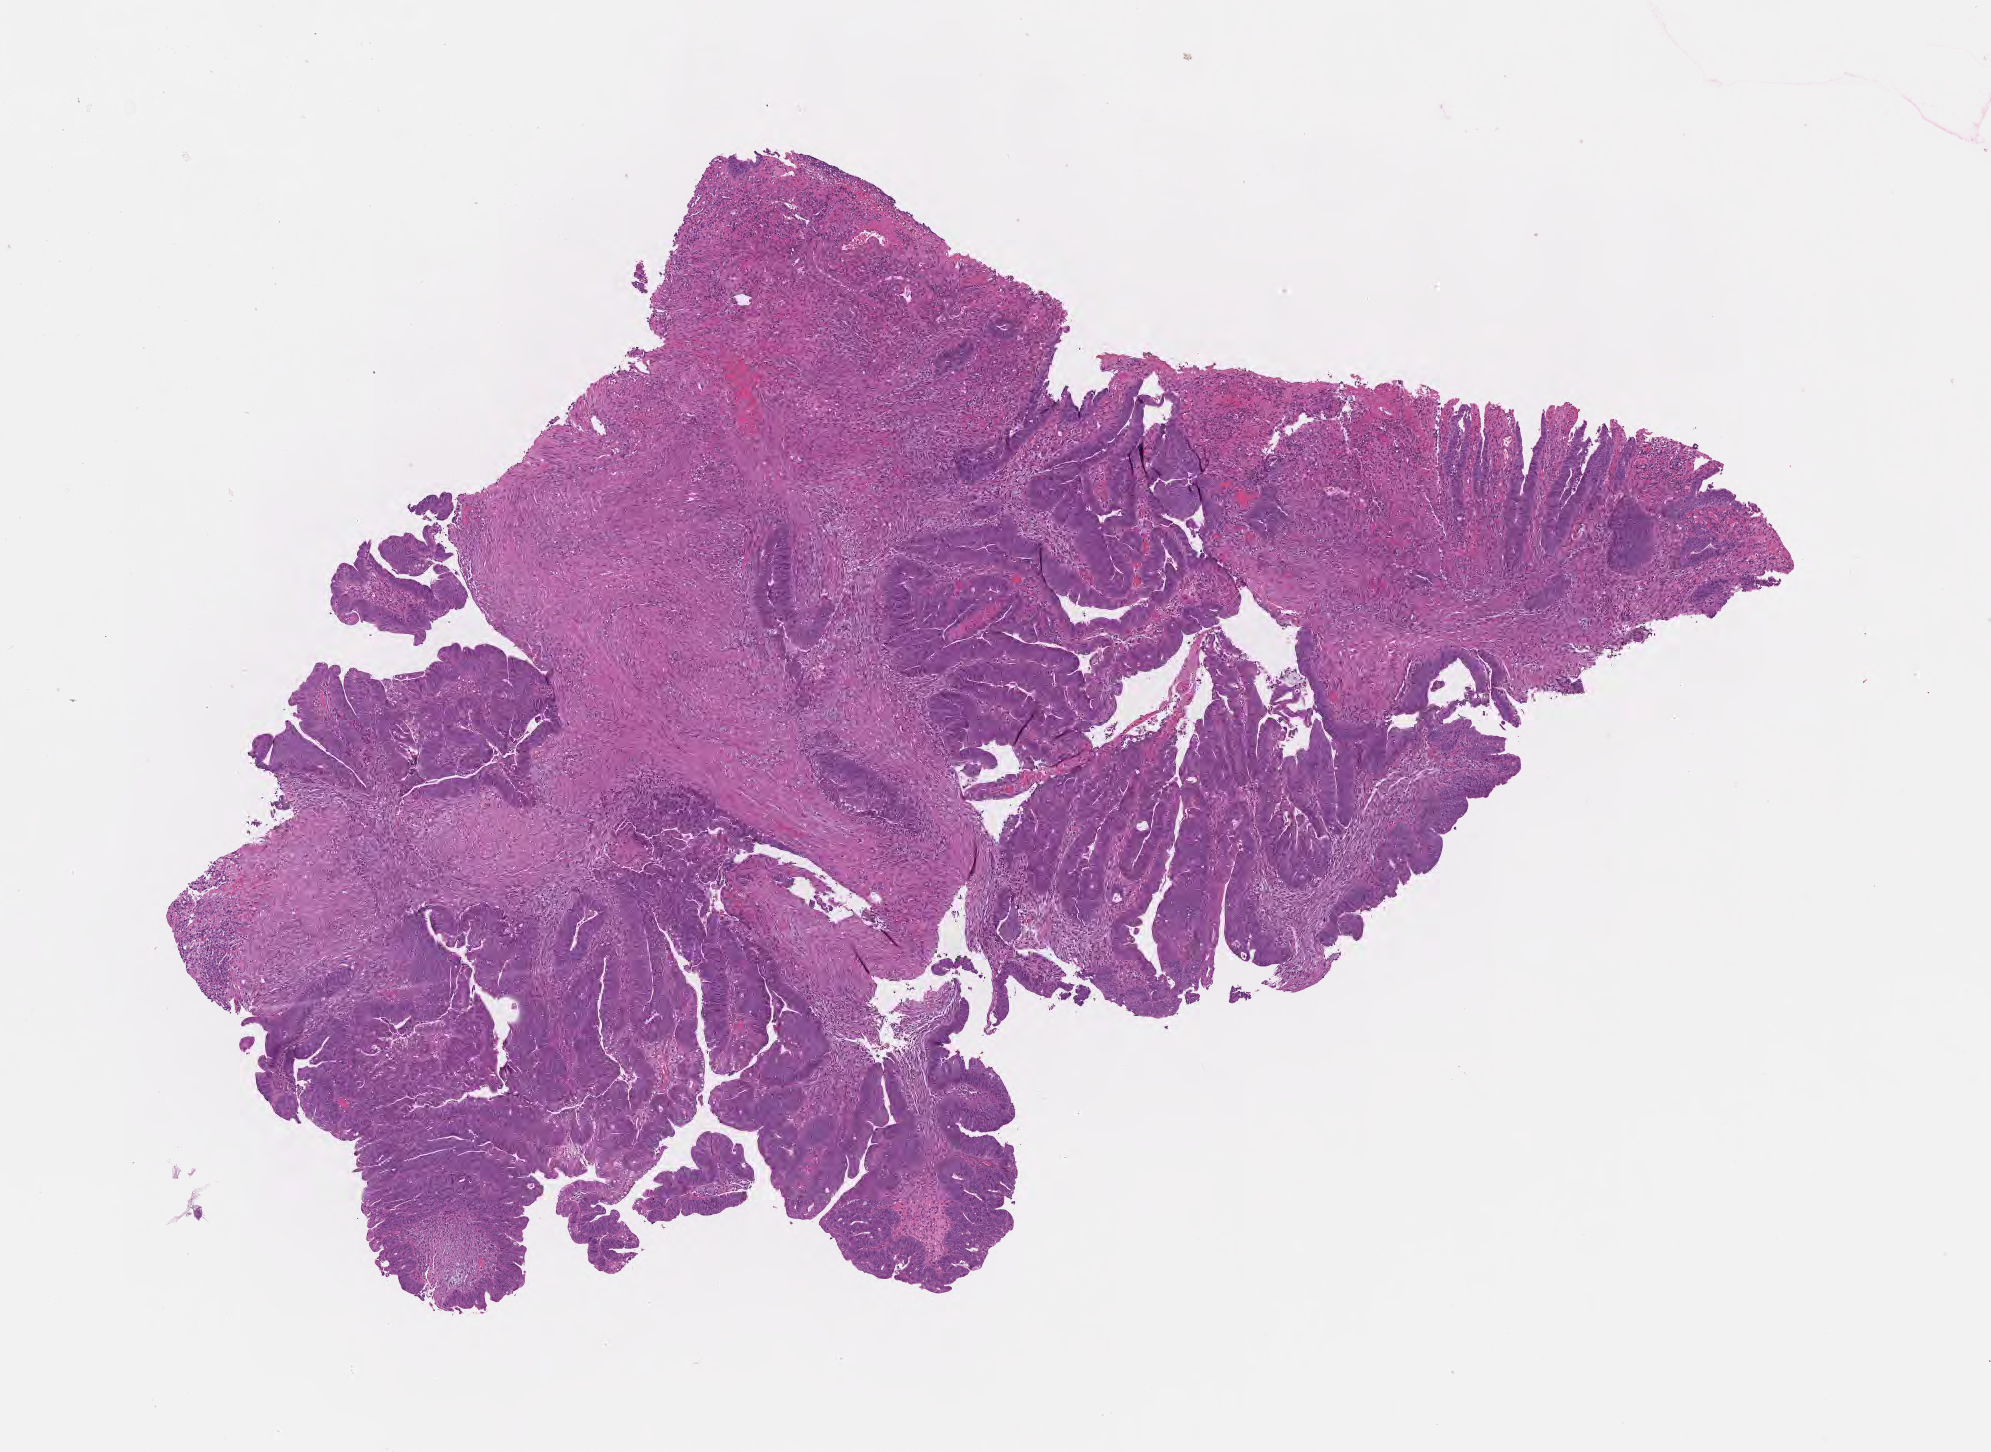
Whole-slide image, hematoxylin and eosin (H&E) stain, whole scanned area (about 8.1 x 5.9 mm) shown as a low-resolution overview; FFPE section; primary tumor; site: sigmoid colon. Male patient; age at initial diagnosis 71 years. Tumor grade: G2 (moderately differentiated). Slide review estimates, as recorded: tumor cells 75%, tumor nuclei 75%, stromal cells 24%, necrosis 1%, normal cells 0%. Inflammatory infiltration, as recorded: lymphocyte infiltration 6%, monocyte infiltration 2%, neutrophil infiltration 8%.
• histologic diagnosis: Adenocarcinoma, NOS
• section: top of the tissue portion
• AJCC pathologic stage: Stage IIA